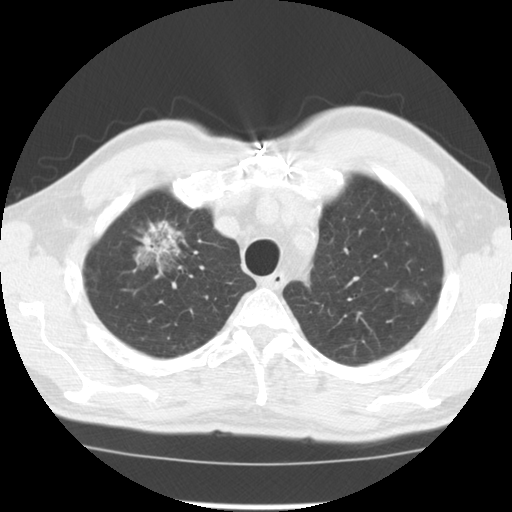
Low-dose screening chest CT, one axial slice. Slice 103 of 128 in the series (ordered by position). Reconstruction kernel STANDARD. 120 kVp. Lung window (W 1500 / L -600 HU). 2.5 mm slice thickness. 512 × 512 image matrix.
Structures marked on this image (expert manual segmentation):
- lesion 1 (tumor, upper lobe of right lung): bounding box <144,229,172,255> (left, top, right, bottom; pixels)